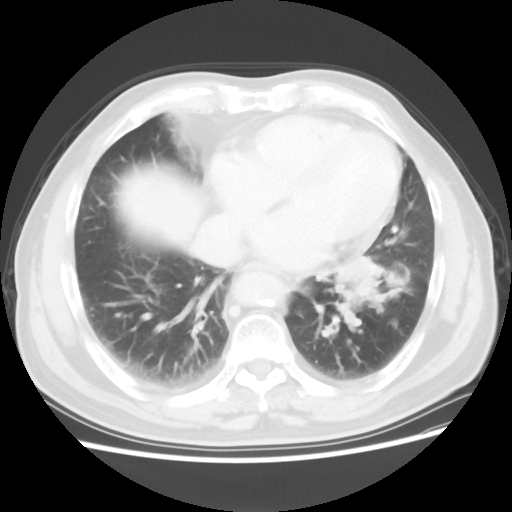
Chest CT, one axial slice. 120 kVp. Lung window (W 1500 / L -600 HU). 512 × 512 image matrix, field of view 360 × 360 mm. Patient: male, 75 years. From the clinical record (not read from this slice): clinical TNM (as recorded): T3 N0 M0.
Annotated regions visible in this slice (rectangle marked by the reading radiologist):
- lung tumour (recorded histology: squamous cell carcinoma): bounding box (x1, y1, x2, y2) in pixels: (327, 252, 397, 324)